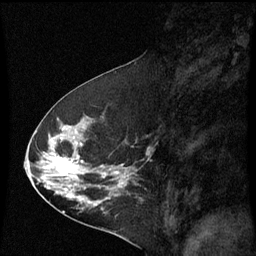
Breast MRI (dynamic contrast-enhanced), one sagittal slice. Slice 30 of 60 in the series (ordered by position). Dynamic contrast-enhanced series, image 2 of 3 at this slice position (ordered by acquisition). 1.5 T. TE 4.2 ms, TR 8.9 ms. 256 × 256 image matrix. Patient: female, 53 years. Case-level facts recorded for this patient, not image findings: setting: breast cancer imaged before/during neoadjuvant chemotherapy; receptor status: HR-positive, HER2-negative.
Structures marked on this image (semi-automatic segmentation, software-assisted and operator-edited):
- analysis volume of interest (the breast-tissue region the enhancement analysis was run in; not a lesion): bounding box <32,100,143,221> (left, top, right, bottom; pixels)
- tumour enhancement mask (voxels above the 70 % enhancement threshold inside the analysis volume of interest): <50,144,129,197>